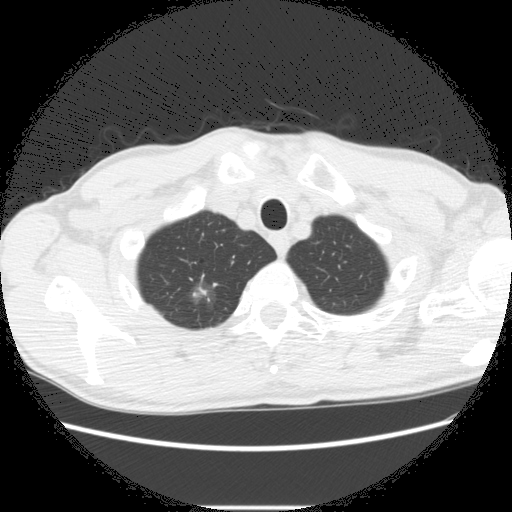
Low-dose screening chest CT, axial slice; second screening round (one year after baseline); lung window (W 1500 / L -600 HU); slice 28 of 282 in the series; 512 × 512 image matrix, field of view 360 × 360 mm. Male participant, aged 66 years at enrolment. Former smoker at enrolment.
Expert-annotated lung lesion, box from (x=173, y=279) to (x=231, y=326) px. The screening reader recorded 5 non-calcified nodules or masses ≥4 mm on this exam (right lower lobe, right upper lobe, right upper lobe, right upper lobe, left lower lobe); which of them this box marks is not recorded. Participant outcome: lung cancer diagnosed 75 days after this screen — adenocarcinoma, NOS, right upper lobe, undifferentiated (G4), stage IA (AJCC 6th edition), 20 mm at pathology.